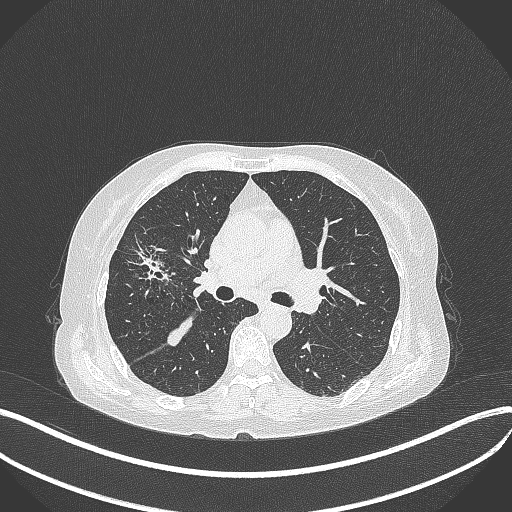
Chest CT, one axial slice; position 237 of 429 along the scan axis; reconstruction kernel B70f; 120 kVp; lung window (W 1500 / L -600 HU); 512 × 512 image matrix, field of view 400 × 400 mm. Patient: female, 69 years. From the clinical record (not read from this slice): clinical TNM (as recorded): T1b N3 M0.
Structures marked on this image (rectangle marked by the reading radiologist):
- lung tumour (recorded histology: small cell carcinoma): box from (x=122, y=236) to (x=173, y=288) px